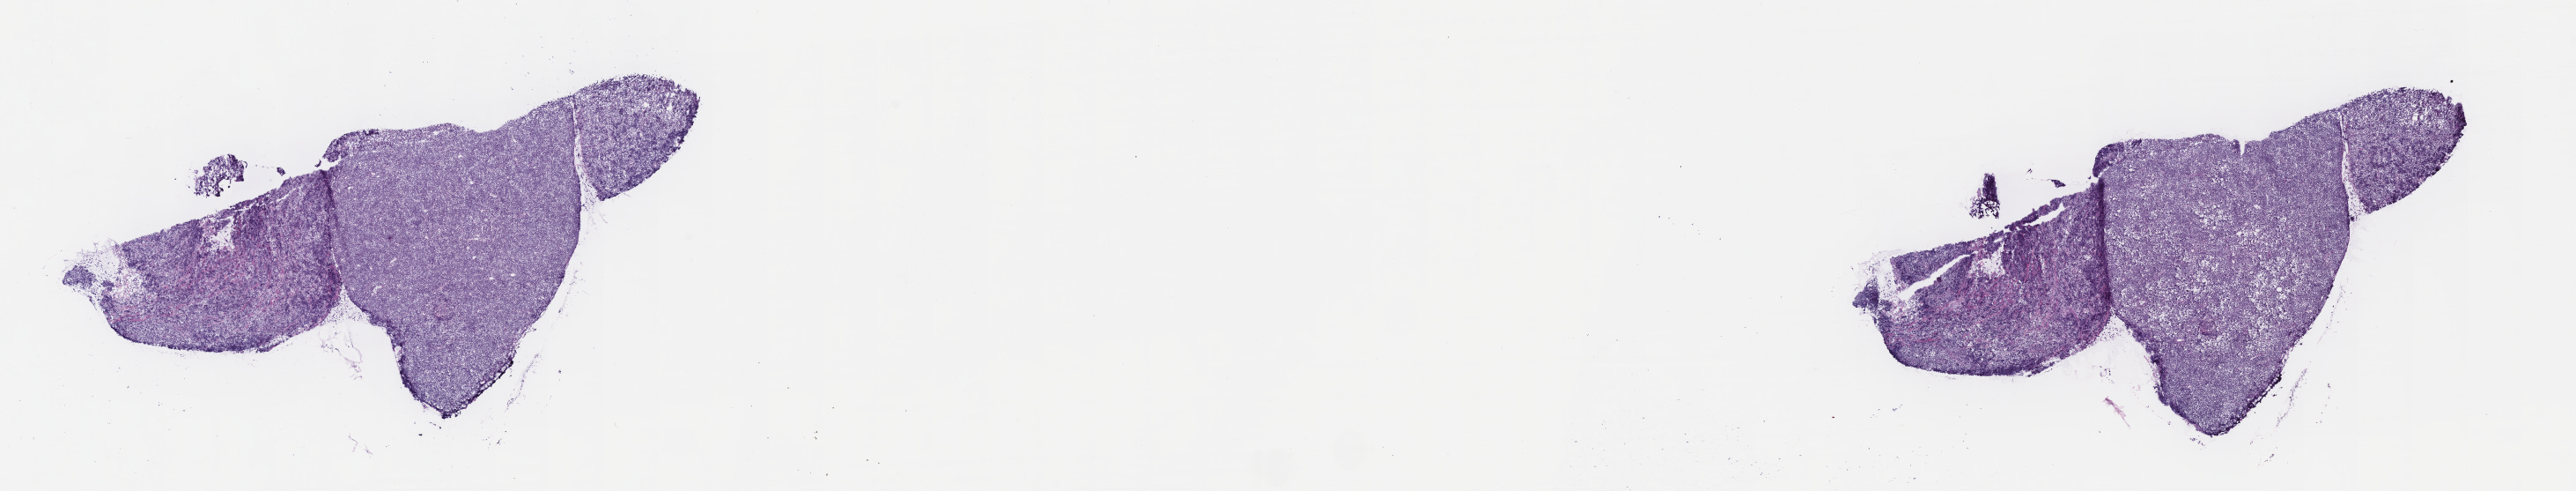
Digitized hematoxylin and eosin (H&E)-stained section — a low-resolution overview of the entire scanned area, about 23.6 x 4.5 mm. Frozen section. Specimen: primary tumor. Site: cranium. Male, age 5 years at initial diagnosis. Slide review estimates, as recorded: tumor cells 90%, tumor nuclei 95%, stromal cells 5%, necrosis 5%, normal cells 0%. Infiltration values recorded for this section: lymphocyte infiltration 70%, monocyte infiltration 15%, neutrophil infiltration 0%.
- diagnosis: Burkitt lymphoma, NOS